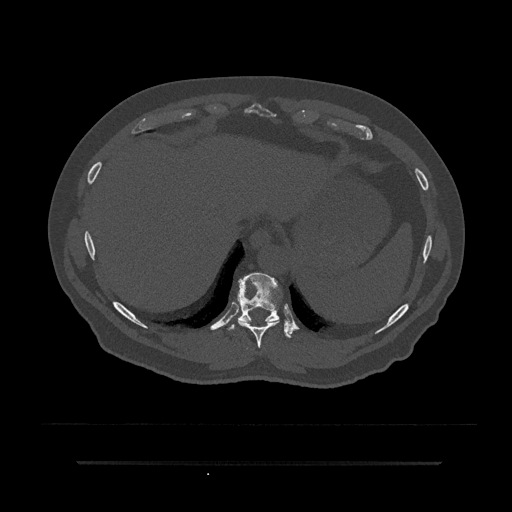
CT including the spine, one axial slice. Slice 353 of 797 in the series (ordered by position). Bone window (W 1800 / L 400 HU). 0.5 mm slice thickness. 512 × 512 image matrix, field of view 464 × 464 mm. Patient: male, 59 years. From the clinical record (not read from this slice): primary cancer: bile ducts.
Structures marked on this image (semi-automatic segmentation, software-assisted and operator-edited):
- T10 vertebra: bounding box (x1, y1, x2, y2) in pixels: (229, 273, 293, 338)
- T9 vertebra: (240, 321, 280, 348)